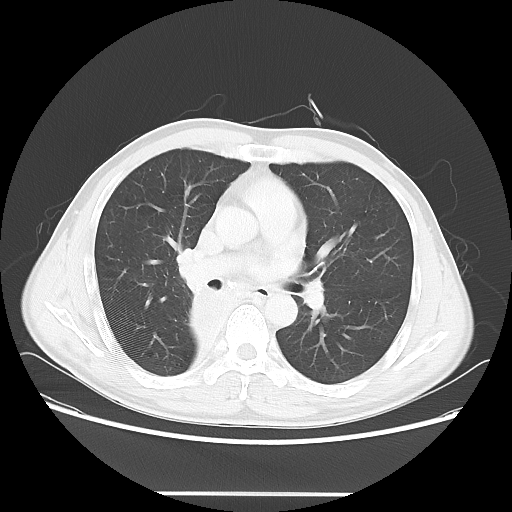
Chest CT, one axial slice. Position 35 of 62 along the scan axis. Reconstruction kernel LUNG. 120 kVp. Lung window (W 1500 / L -600 HU). 5 mm slice thickness. 512 × 512 image matrix, field of view 393 × 393 mm. Patient: male, 47 years. Case-level facts recorded for this patient, not image findings: clinical TNM (as recorded): T2 N0 M0; histopathological grade: G2.
Structures marked on this image (rectangle marked by the reading radiologist):
- lung tumour (recorded histology: squamous cell carcinoma): bounding box [x1, y1, x2, y2] px = [187, 285, 250, 343]